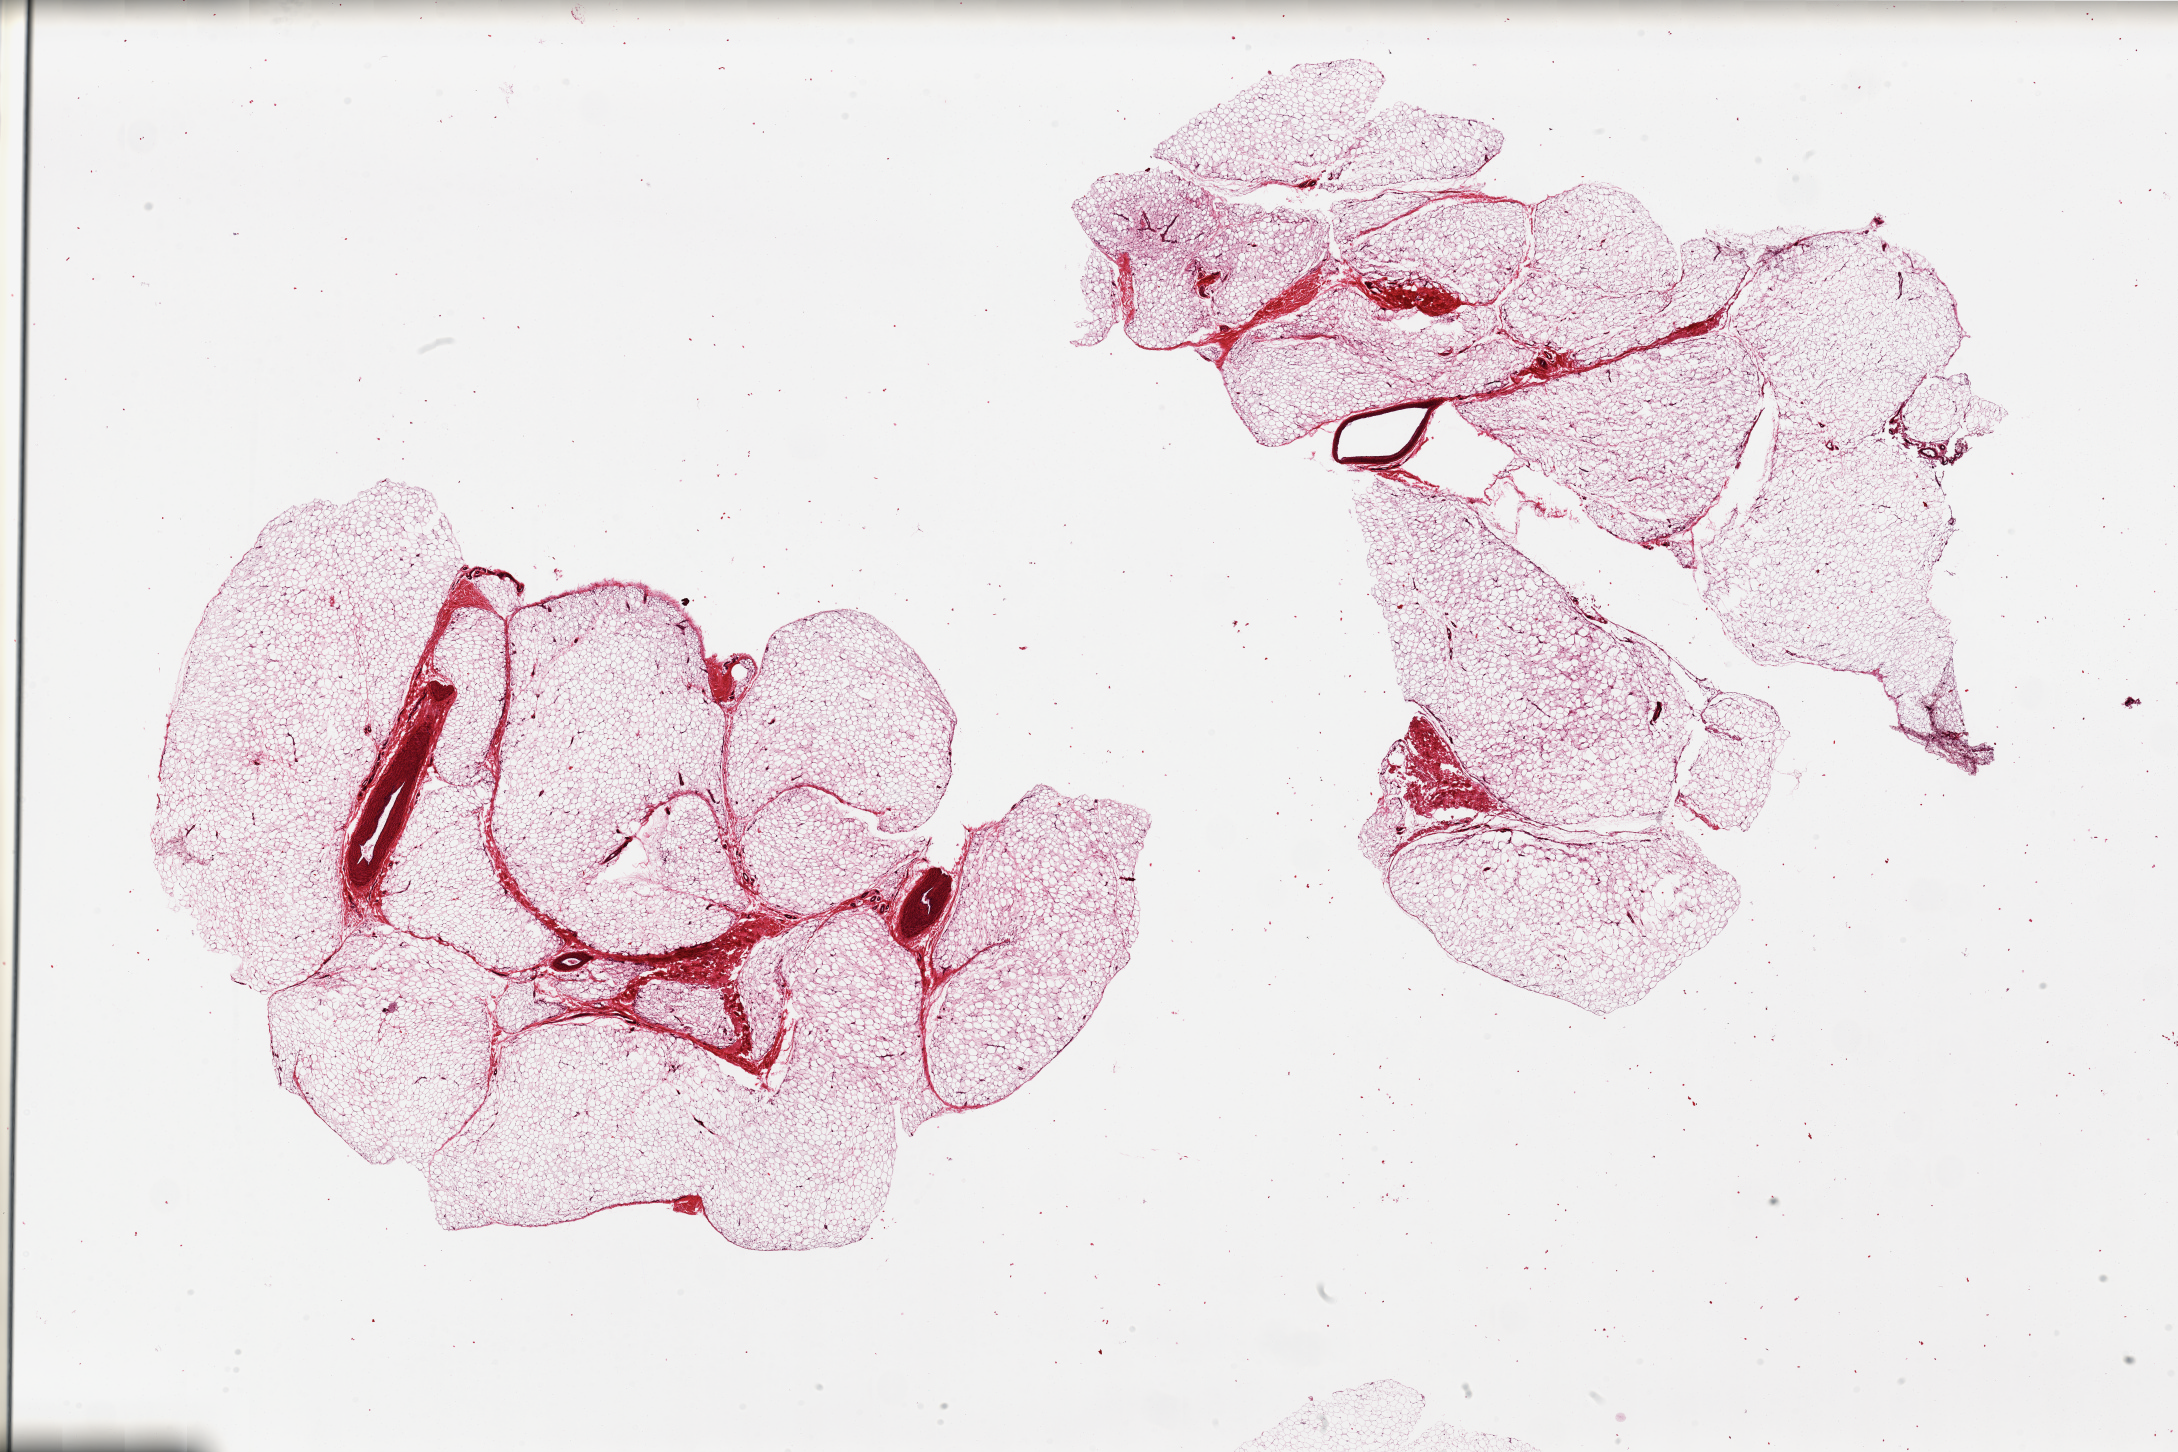
Digitized hematoxylin and eosin (H&E)-stained section, brightfield — low-resolution overview of the scanned area, about 34.5 x 23.0 mm; PAXgene-fixed, paraffin-embedded tissue; target tissue: adipose tissue; donor tissue sample. Male donor.
Pathologist's review note for this sample: 2 pieces, well preserved, each is ~5% vascular/fibrous components.